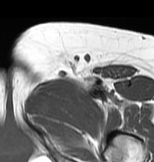
MRI of an extremity soft-tissue mass, one axial slice; slice 49 of 83 in the series (ordered by position); MR volume resampled by the dataset authors to the PET/CT grid (not the native acquisition matrix); 154 × 162 image matrix. Female patient. From the clinical record (not read from this slice): histological type: myxofibrosarcoma; grade: intermediate; site of the primary tumour: left thigh.
Structures marked on this image (expert contour drawn on MRI and transferred to this co-registered scan by the dataset authors):
- gross tumour volume including surrounding oedema: bounding box [x1, y1, x2, y2] px = [28, 73, 121, 115]